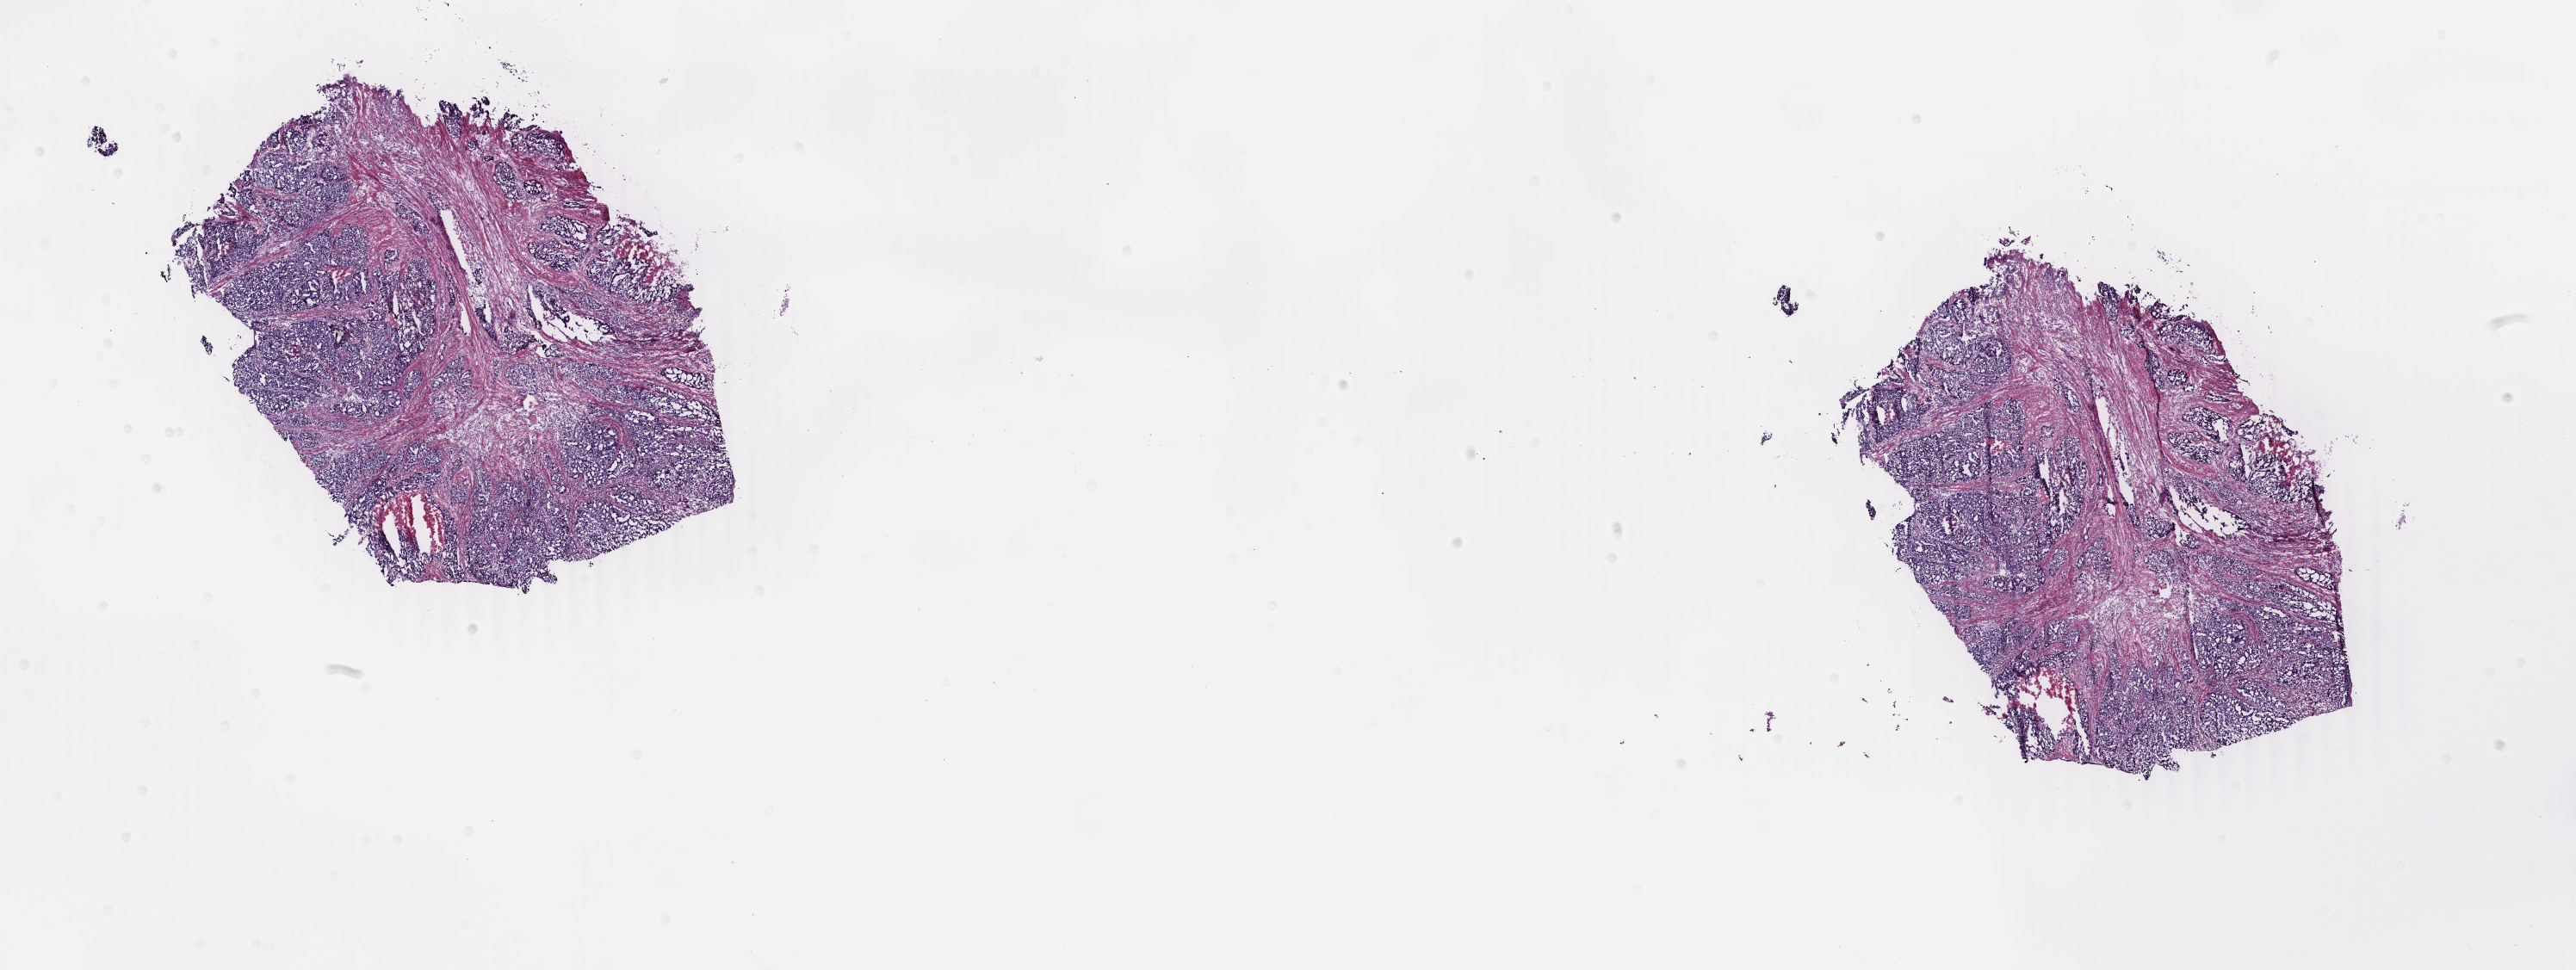
Digitized H&E-stained tissue section (whole slide), shown as a low-resolution overview of the whole scanned area (about 23.8 x 9.0 mm), frozen section from the bottom of the tissue portion, primary tumour sample from the uterus. Female patient; age at initial diagnosis 73 years.
Diagnosis: Endometrioid adenocarcinoma, NOS (endometrium).